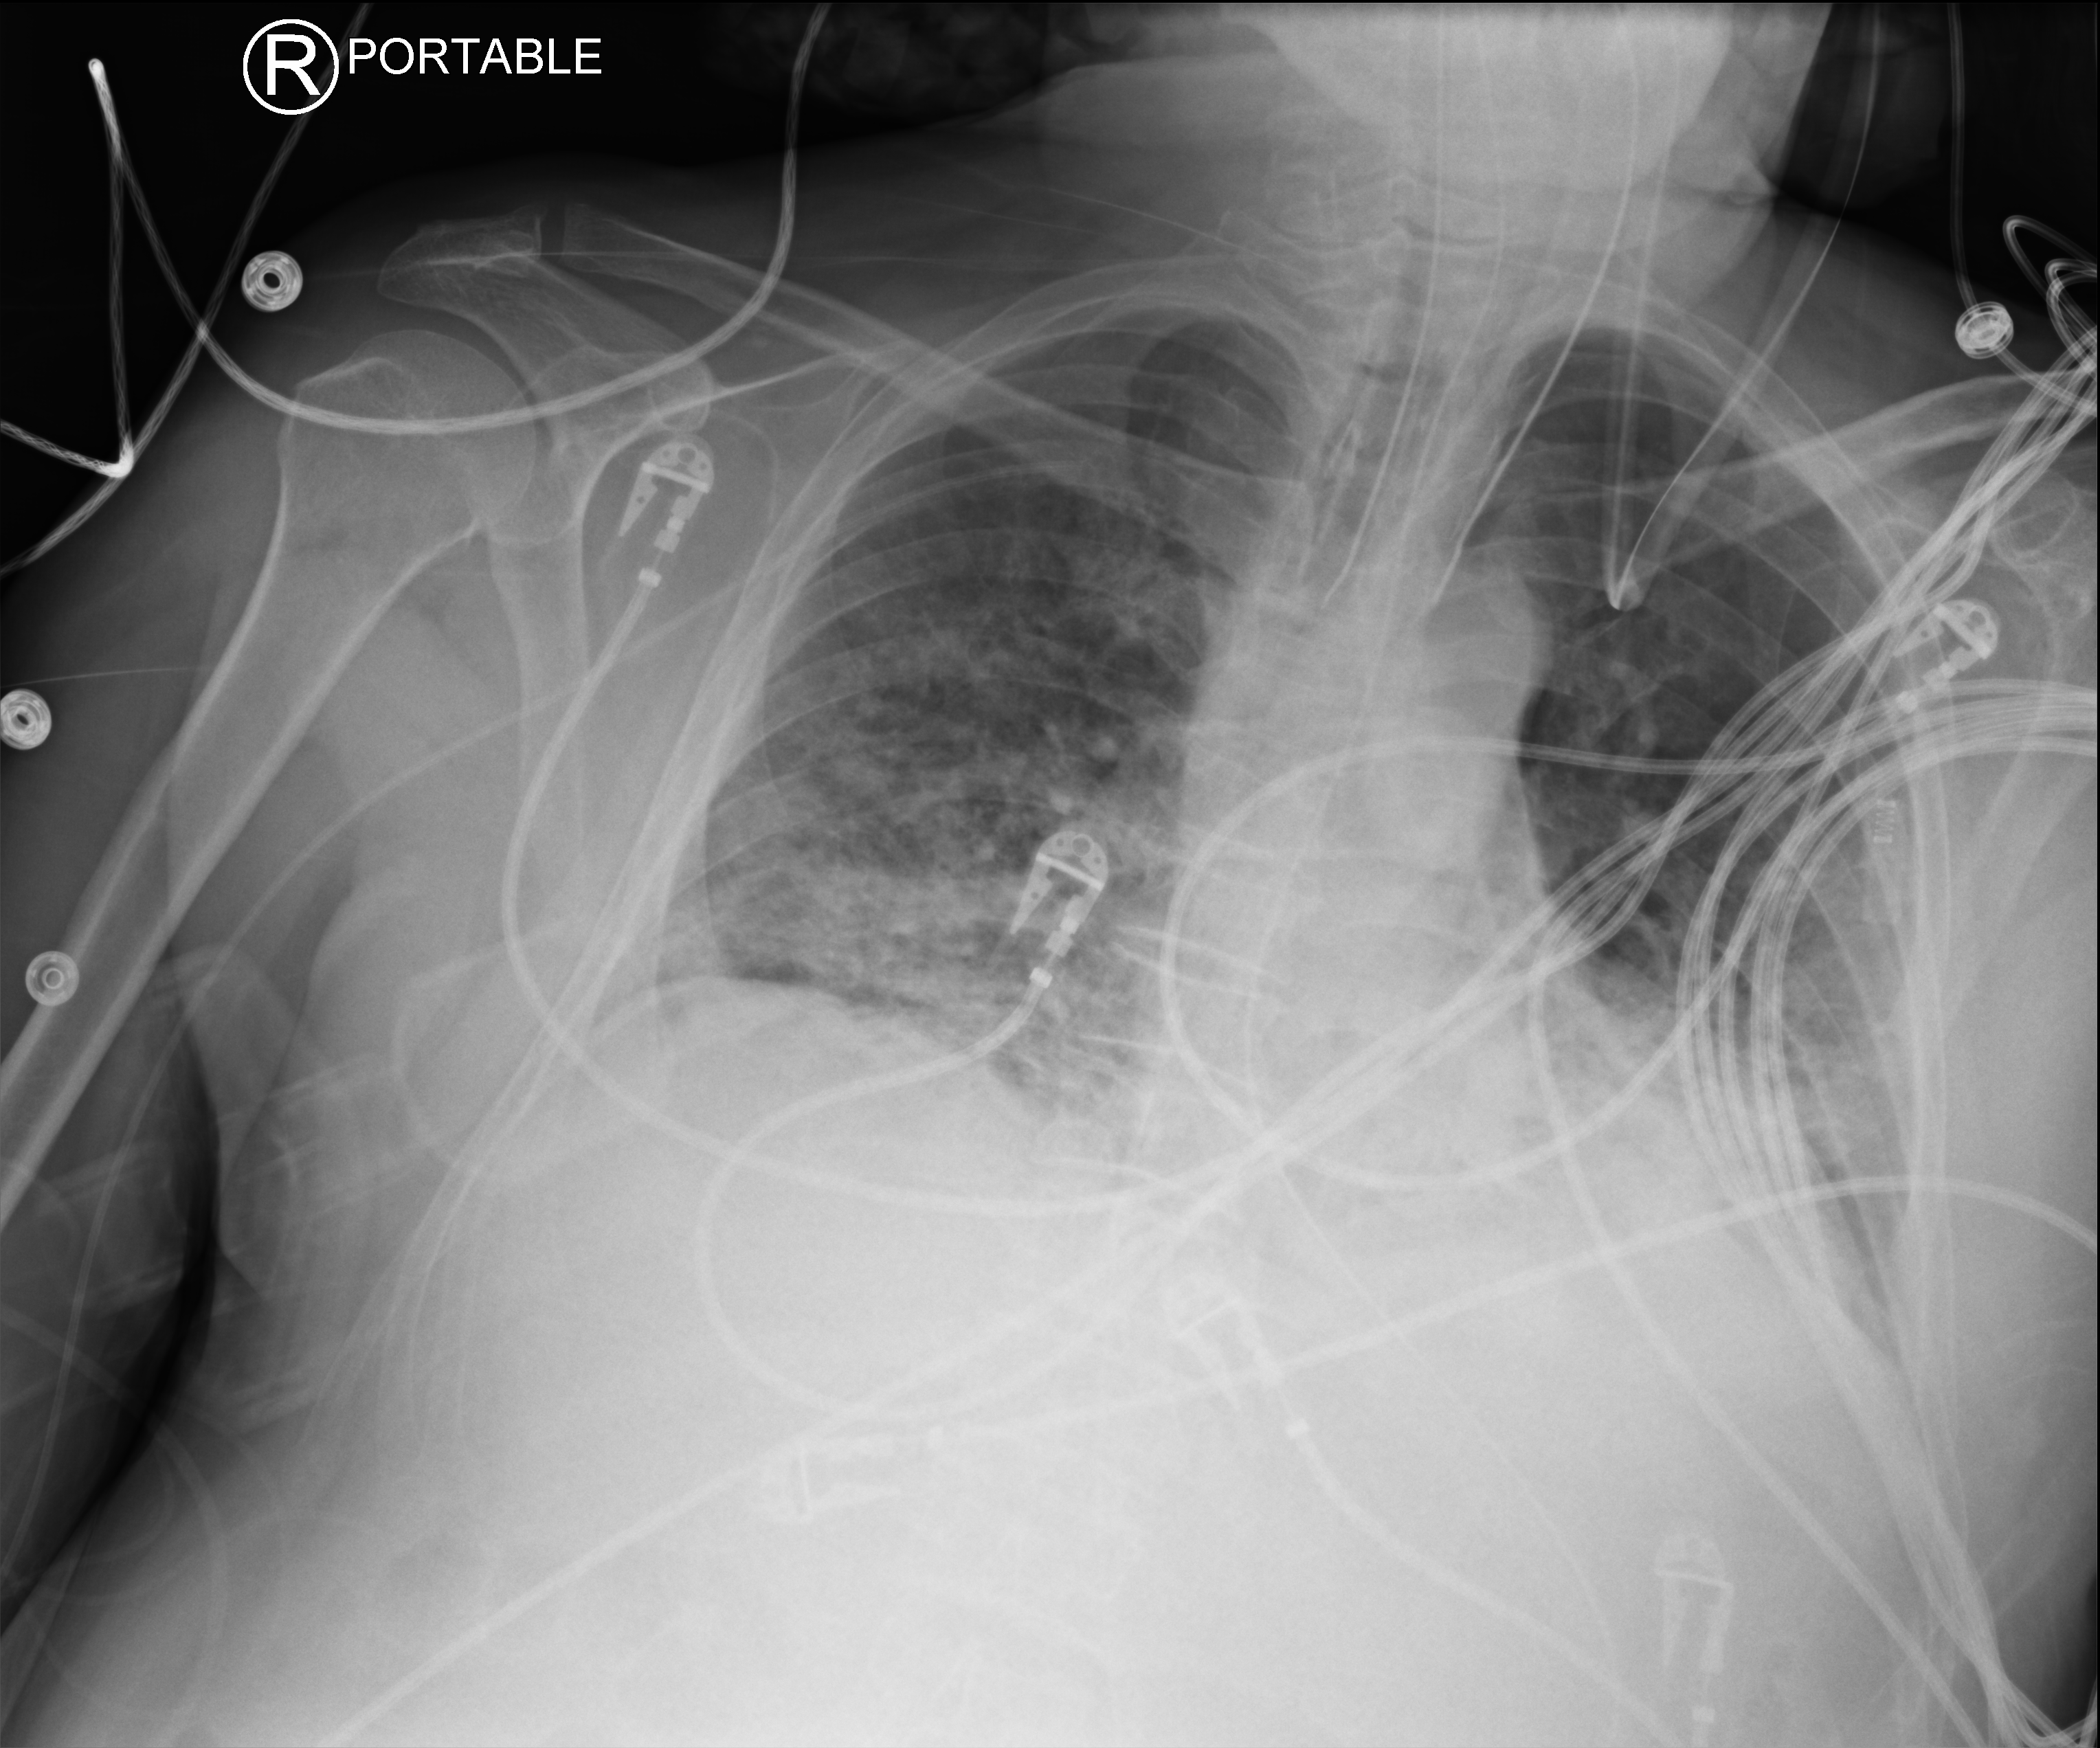
Bedside chest radiograph (computed radiography). Male patient hospitalised with COVID-19, age 60–74 years.
From the hospital-stay record, not from the radiograph (when in the stay this image was taken is not recorded): admitted to intensive care during this hospital stay: yes.